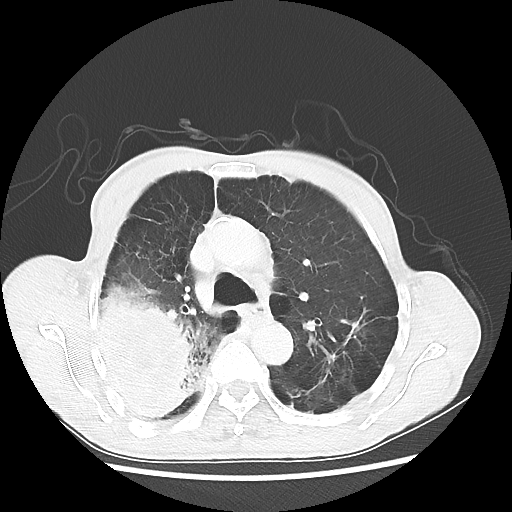
Chest CT, one axial slice. Position 37 of 58 along the scan axis. Reconstruction kernel LUNG. 100 kVp. Lung window (W 1500 / L -600 HU). 512 × 512 image matrix, field of view 351 × 351 mm. Patient: male, 75 years. From the clinical record (not read from this slice): clinical TNM (as recorded): T4 N1 M1.
Outlined on this slice (rectangle marked by the reading radiologist):
- lung tumour (recorded histology: adenocarcinoma): bounding box [x1, y1, x2, y2] px = [90, 280, 207, 420]